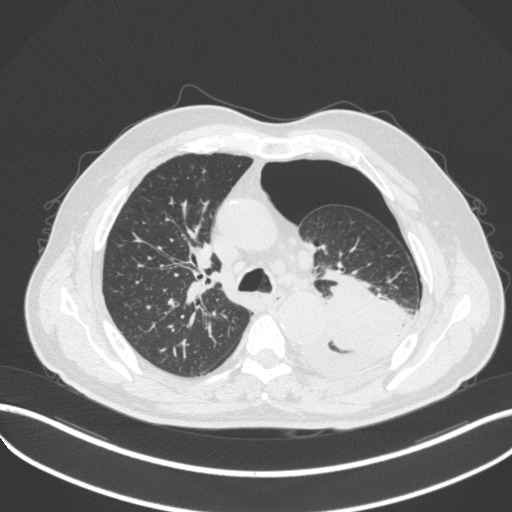
Chest CT, one axial slice. Slice 346 of 466 in the series (ordered by position). Reconstruction kernel B31f. Lung window (W 1500 / L -600 HU). 512 × 512 image matrix. Patient: male, 76 years. From the clinical record (not read from this slice): clinical TNM (as recorded): T3 N0 M1b.
Annotated regions visible in this slice (bounding box drawn by a radiologist):
- lung tumour (recorded histology: adenocarcinoma): bounding box [x1, y1, x2, y2] px = [296, 271, 415, 377]